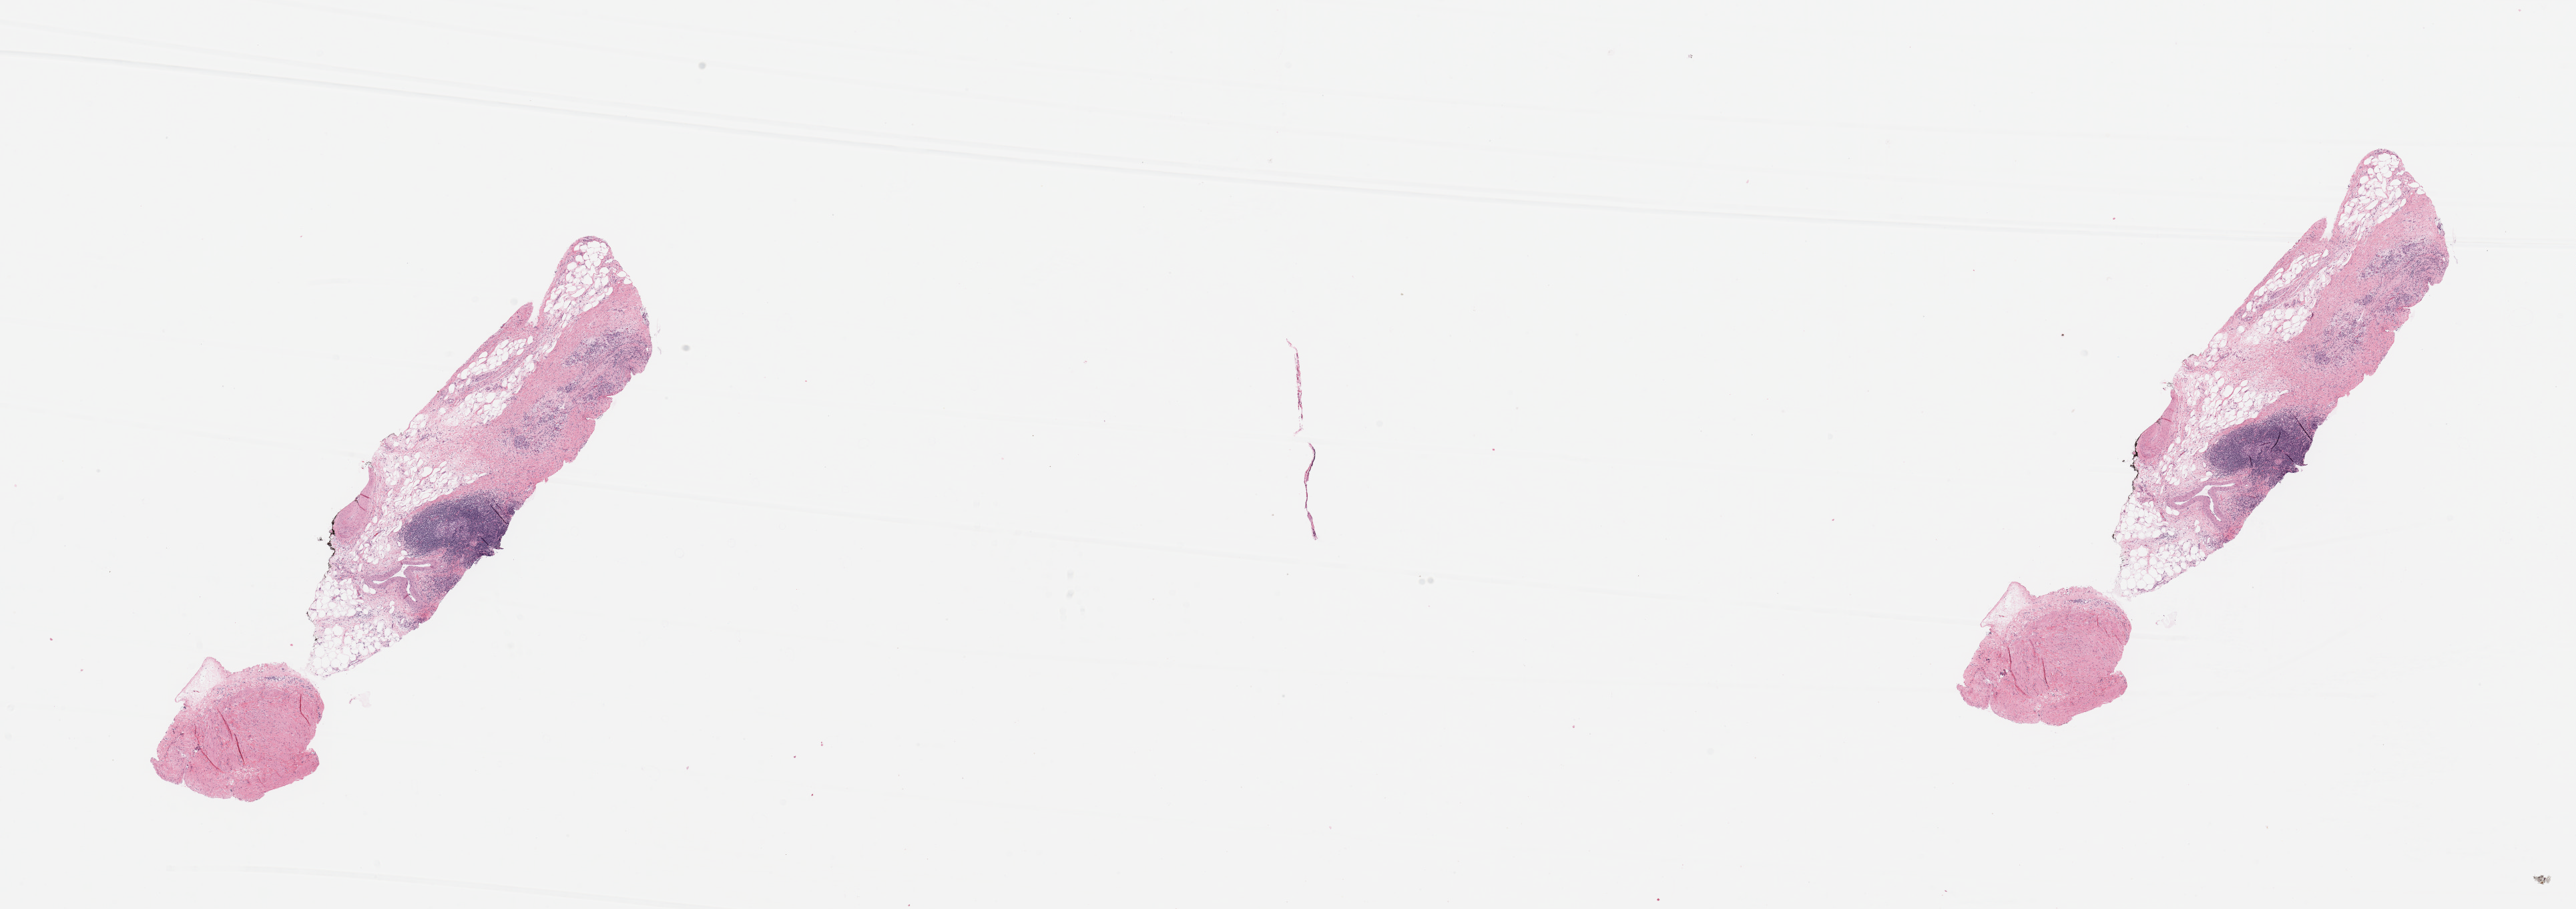
Whole-slide histology image, H&E, whole scanned area (about 30.5 x 10.8 mm, from a 20x scan) shown as a low-resolution overview, pancreas, tumour tissue. Male, 68 y/o.
* patient diagnosis (cohort enrolment): ductal adenocarcinoma (pancreas)
* primary tumour site (as recorded): tail